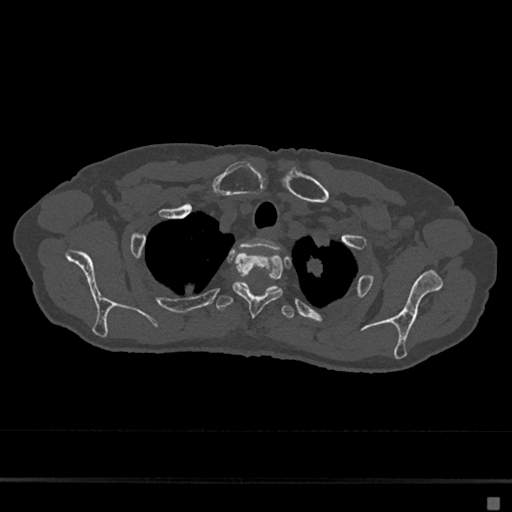
CT including the spine, one axial slice. Position 568 of 797 along the scan axis. Reconstruction kernel Br40s/3. 120 kVp. Bone window (W 1800 / L 400 HU). 0.5 mm slice thickness. 512 × 512 image matrix. Patient: female, 68 years. Case-level facts recorded for this patient, not image findings: primary cancer: renal.
Structures marked on this image (semi-automatically segmented with operator editing):
- T1 vertebra: bounding box <240,239,279,251> (left, top, right, bottom; pixels)
- T2 vertebra: <232,252,283,316>
- T3 vertebra: <216,281,295,319>